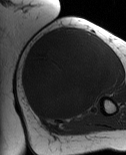
MRI of an extremity soft-tissue mass, one axial slice. Position 37 of 86 along the scan axis. MR volume resampled by the dataset authors to the PET/CT grid (not the native acquisition matrix). 126 × 155 image matrix, field of view 123 × 151 mm. Female patient. Case-level facts recorded for this patient, not image findings: histological type: pleiomorphic leiomyosarcoma; grade: high; site of the primary tumour: left biceps.
Outlined on this slice (expert contour drawn on MRI and transferred to this co-registered scan by the dataset authors):
- gross tumour volume including surrounding oedema: bounding box [x1, y1, x2, y2] px = [22, 26, 112, 121]
- gross tumour volume (mass): [22, 28, 112, 121]